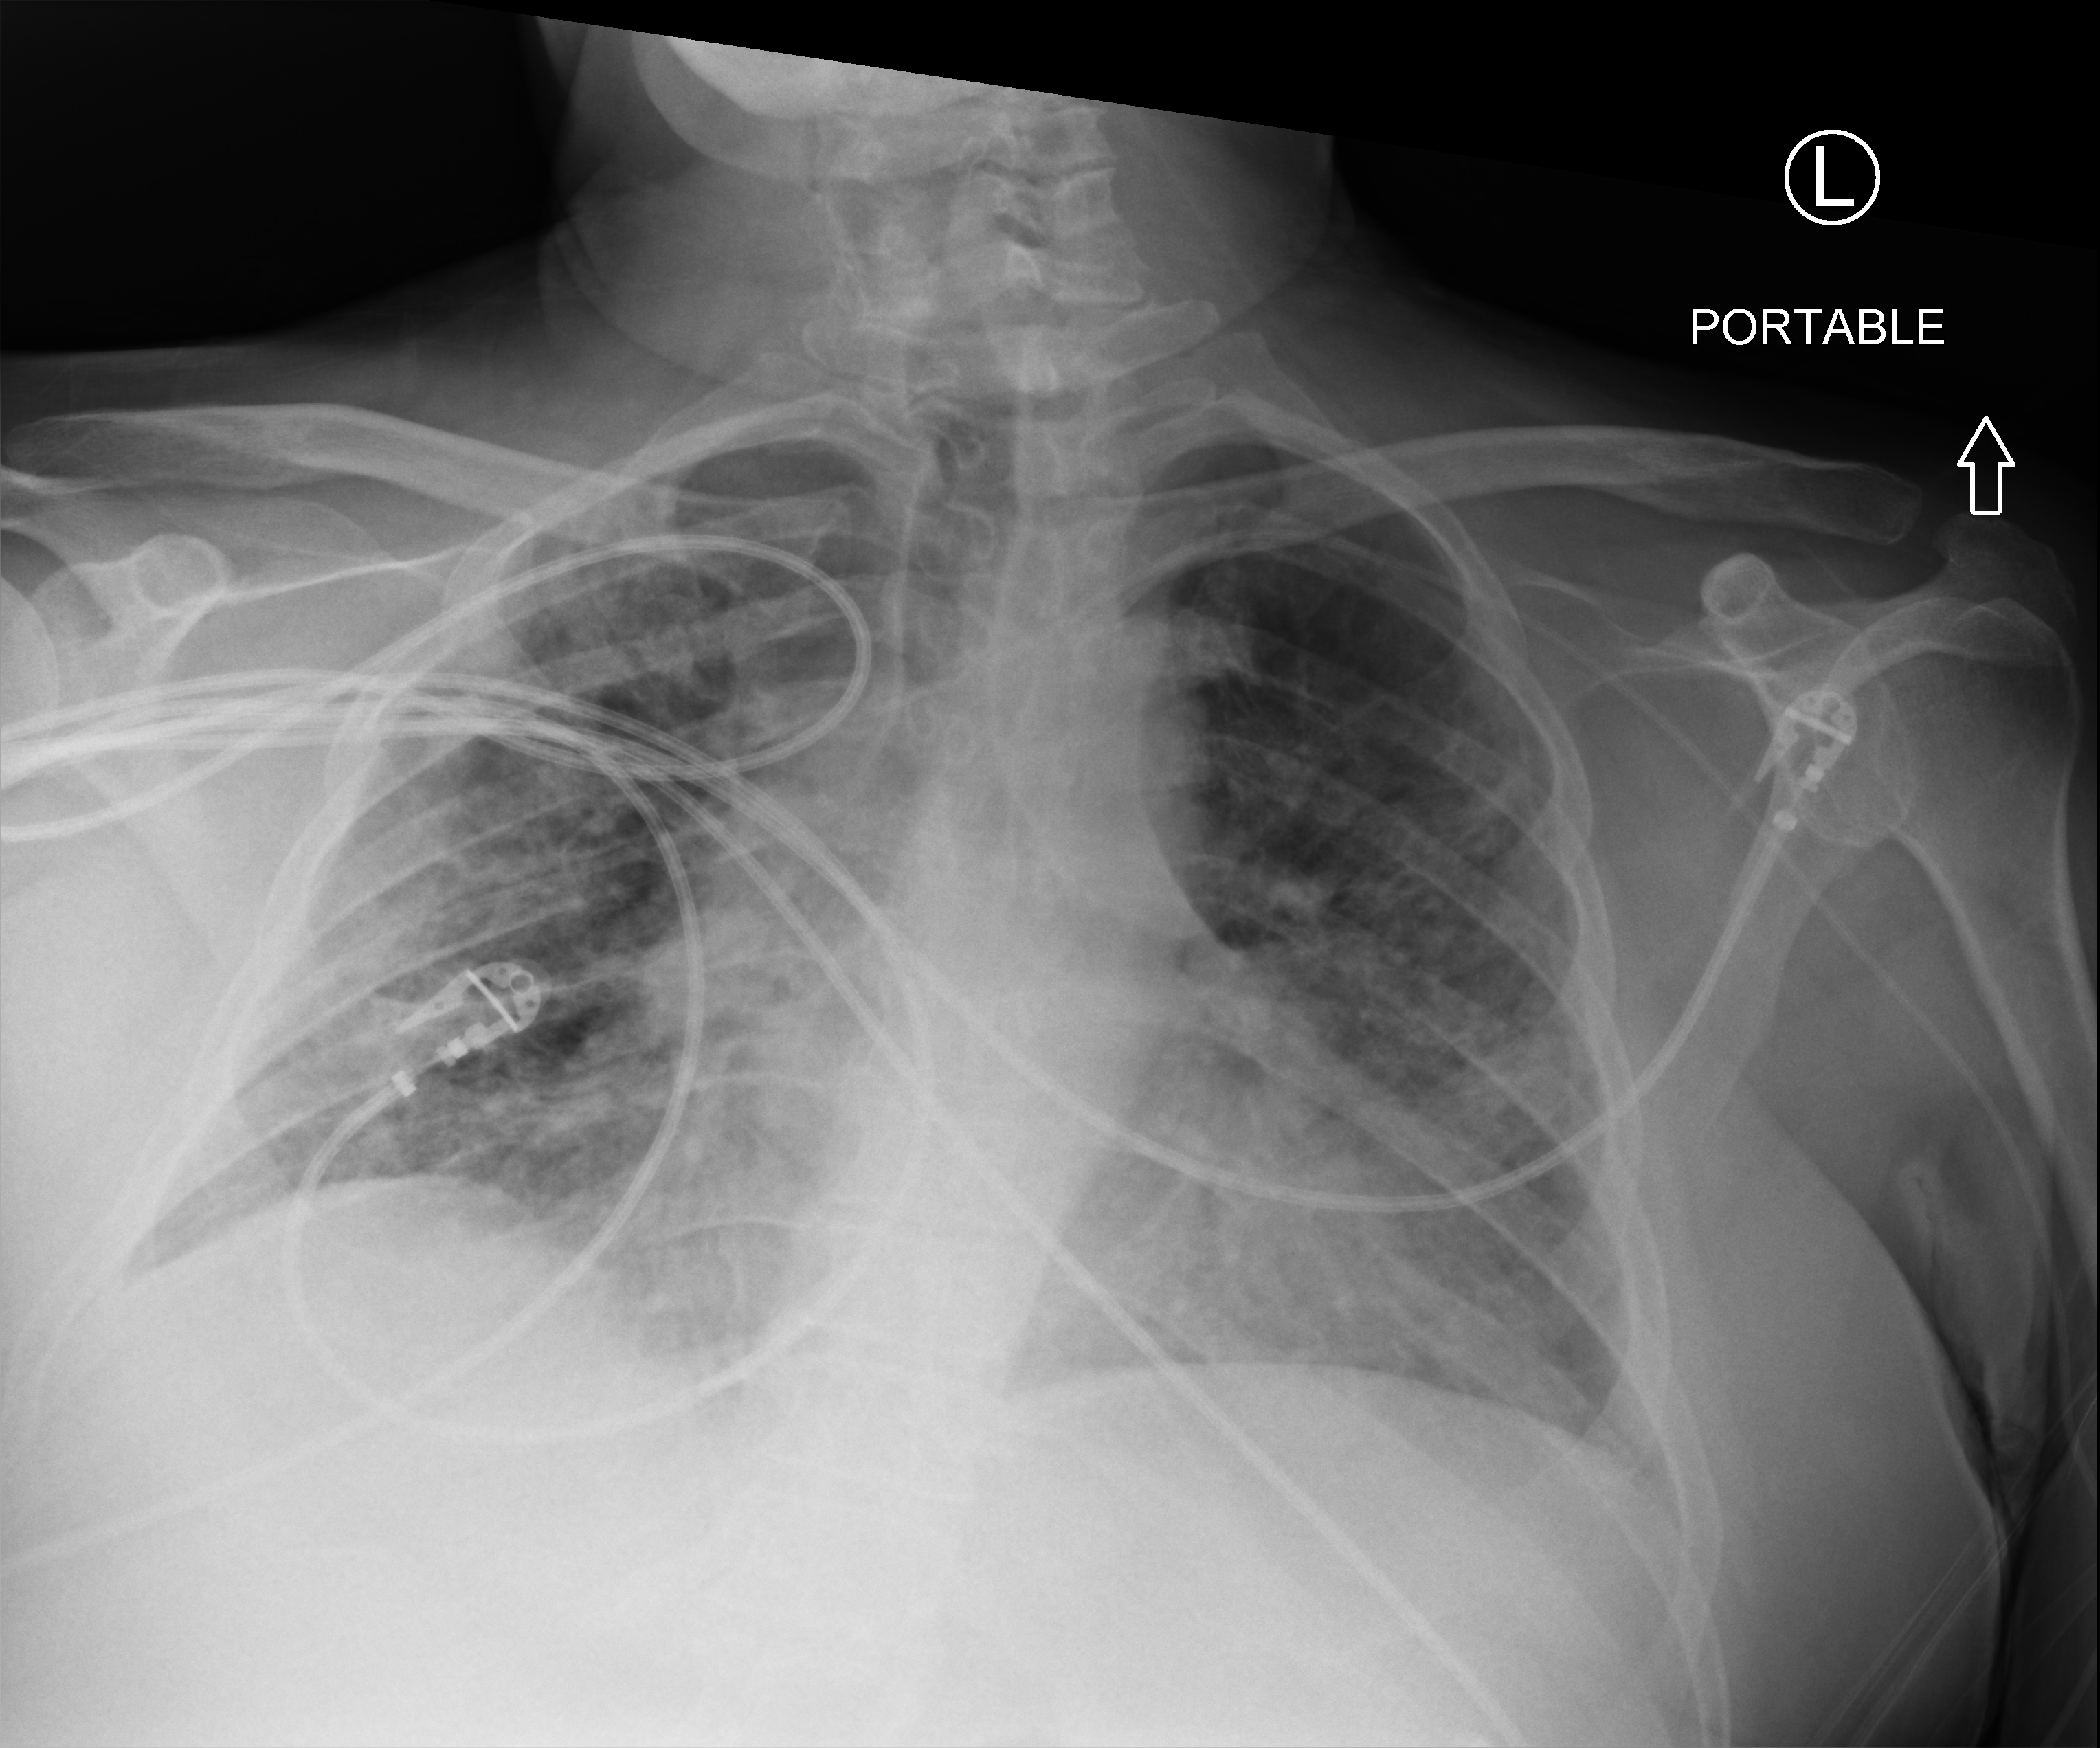
Chest X-ray (portable). Male patient hospitalised with COVID-19, age 18–59 years.
Admission-level facts for this patient (not findings on this image; timing relative to this image not recorded):
- admitted to intensive care during this hospital stay: yes